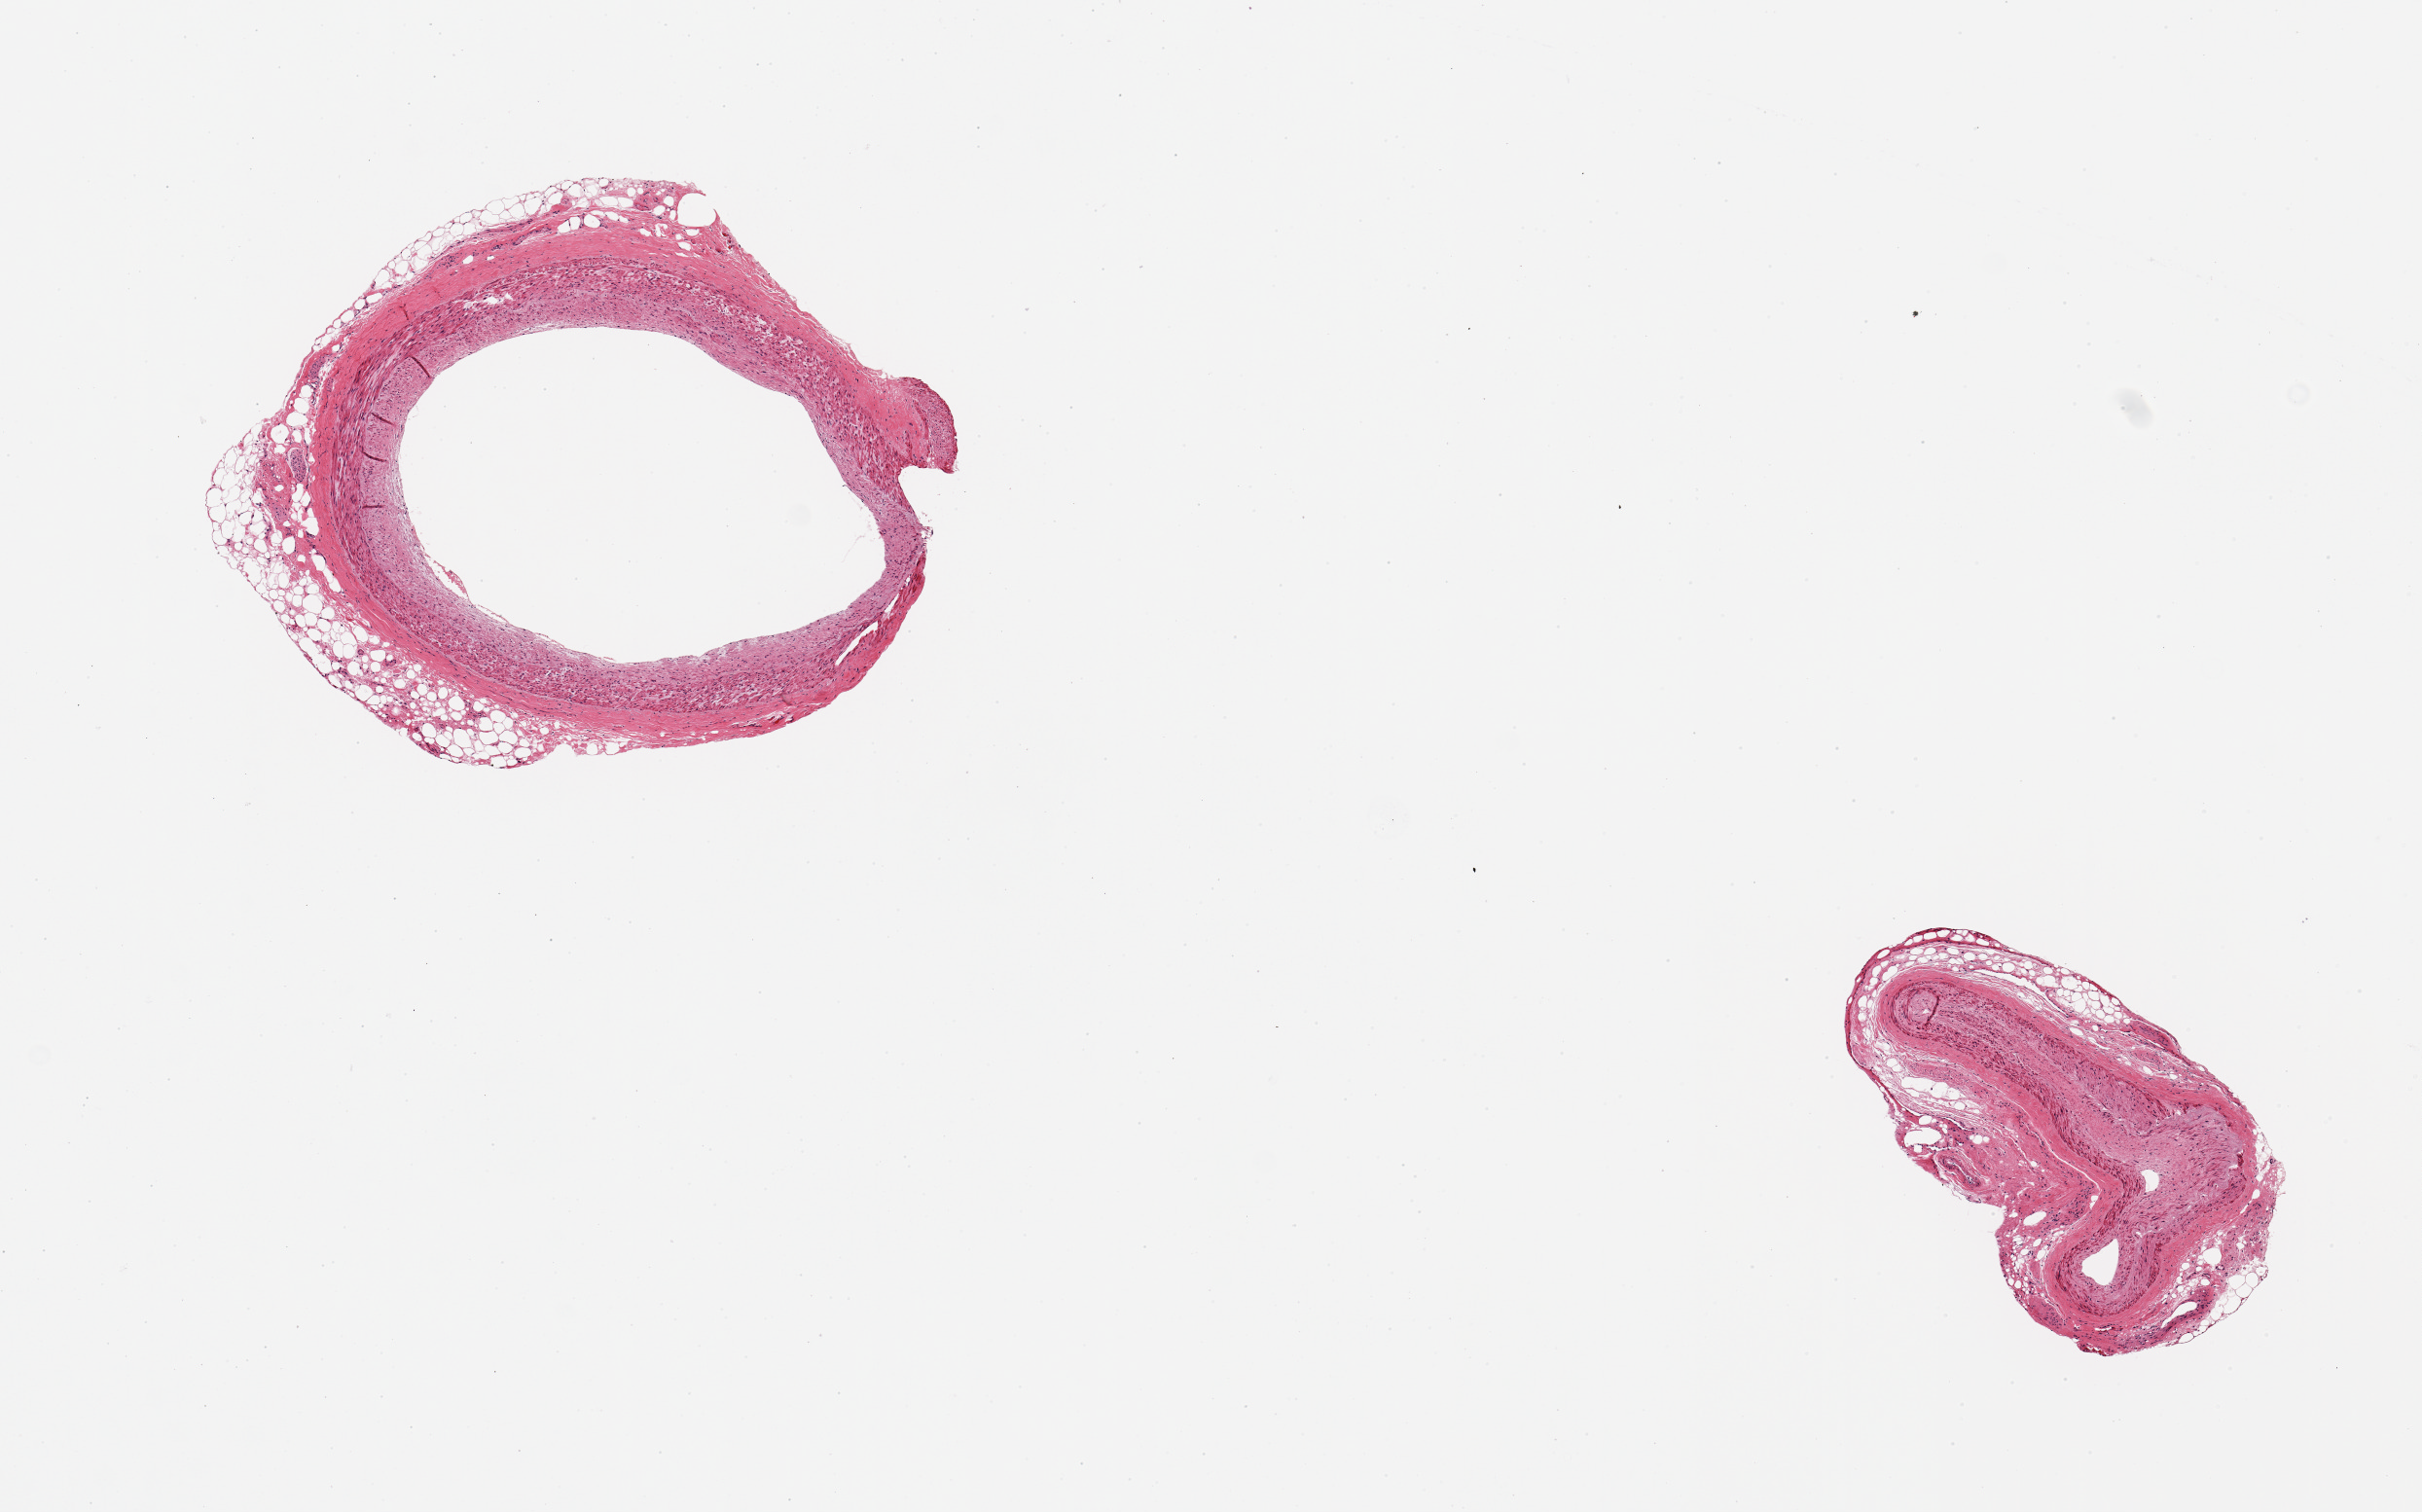
Haematoxylin and eosin whole-slide image — shown as a low-resolution overview of the whole scanned area (about 9.8 x 6.1 mm), PAXgene-fixed paraffin-embedded (PFPE) section, sampled site (target tissue): coronary artery, donor tissue sample.
* pathologist's review note for this sample: 2 pieces; 30% perivascular fat; small amount of plaque